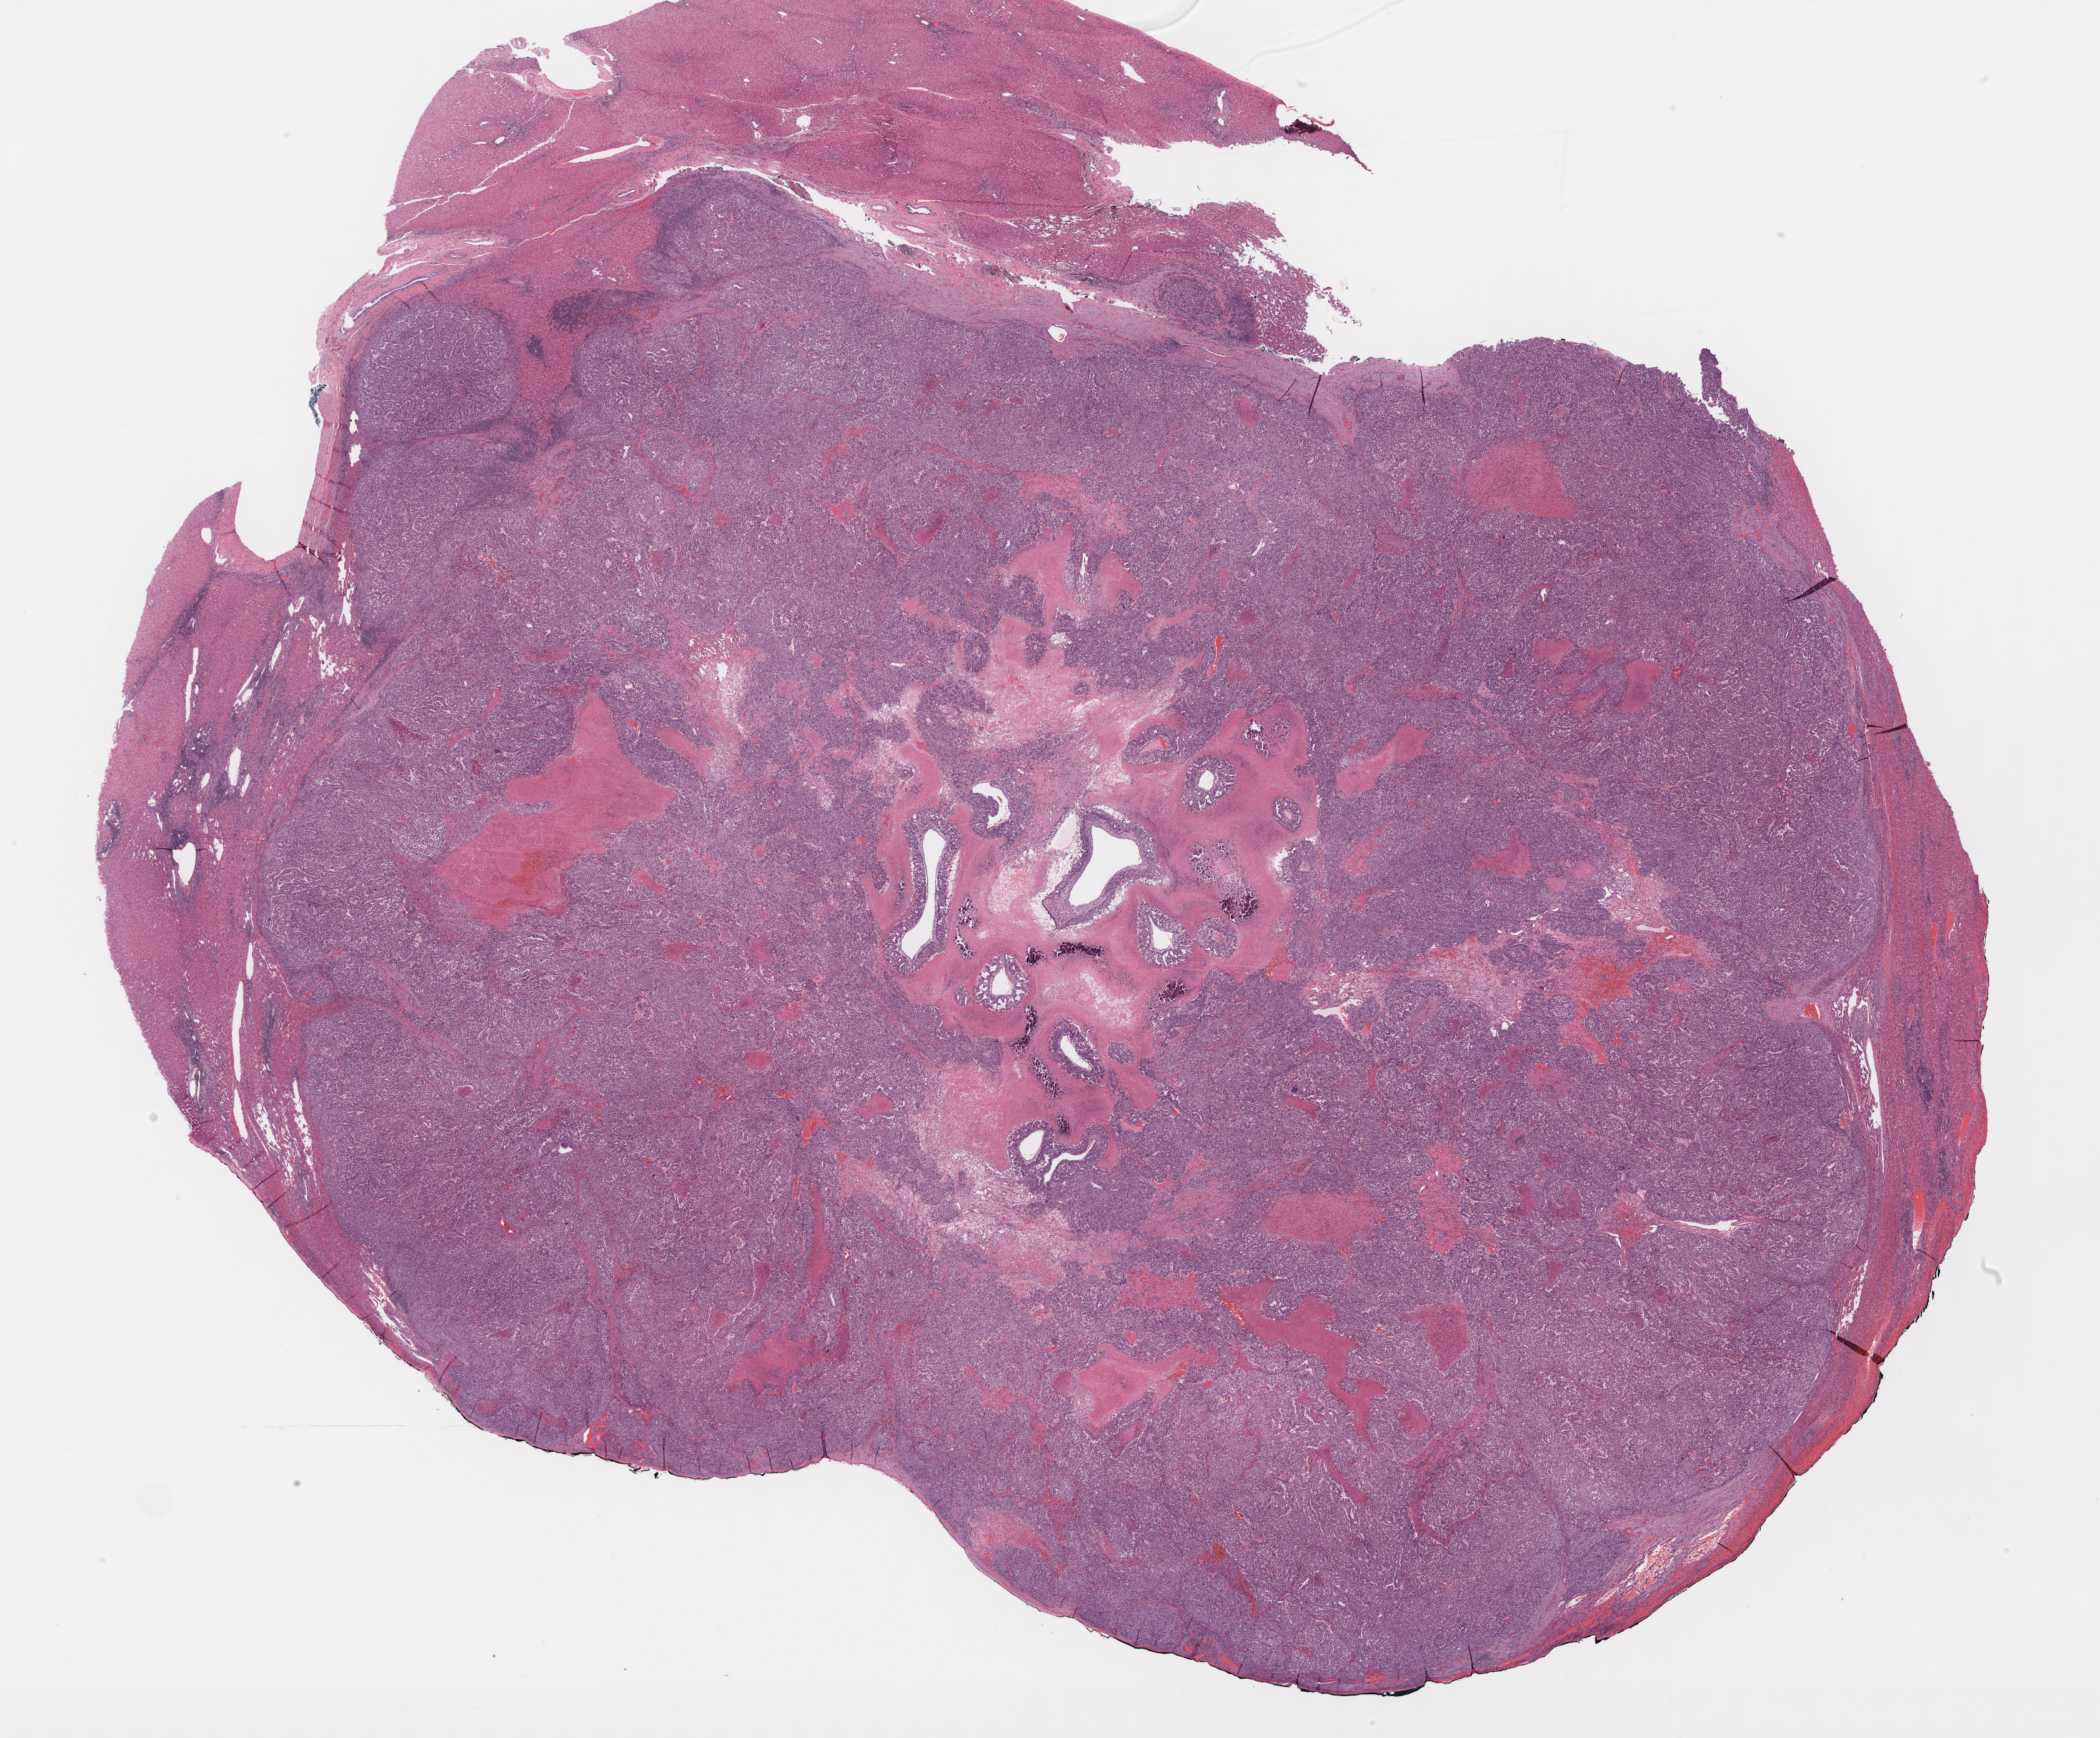
Digitized Hematoxylin and eosin (H&E) stained tissue section (whole slide), whole scanned area (about 27.2 x 22.5 mm) shown as a low-resolution overview. Formalin-fixed paraffin-embedded (FFPE) diagnostic section. Primary tumour sample from the liver. Male, age 38 years at initial diagnosis.
Diagnosis: Hepatocellular carcinoma, NOS.